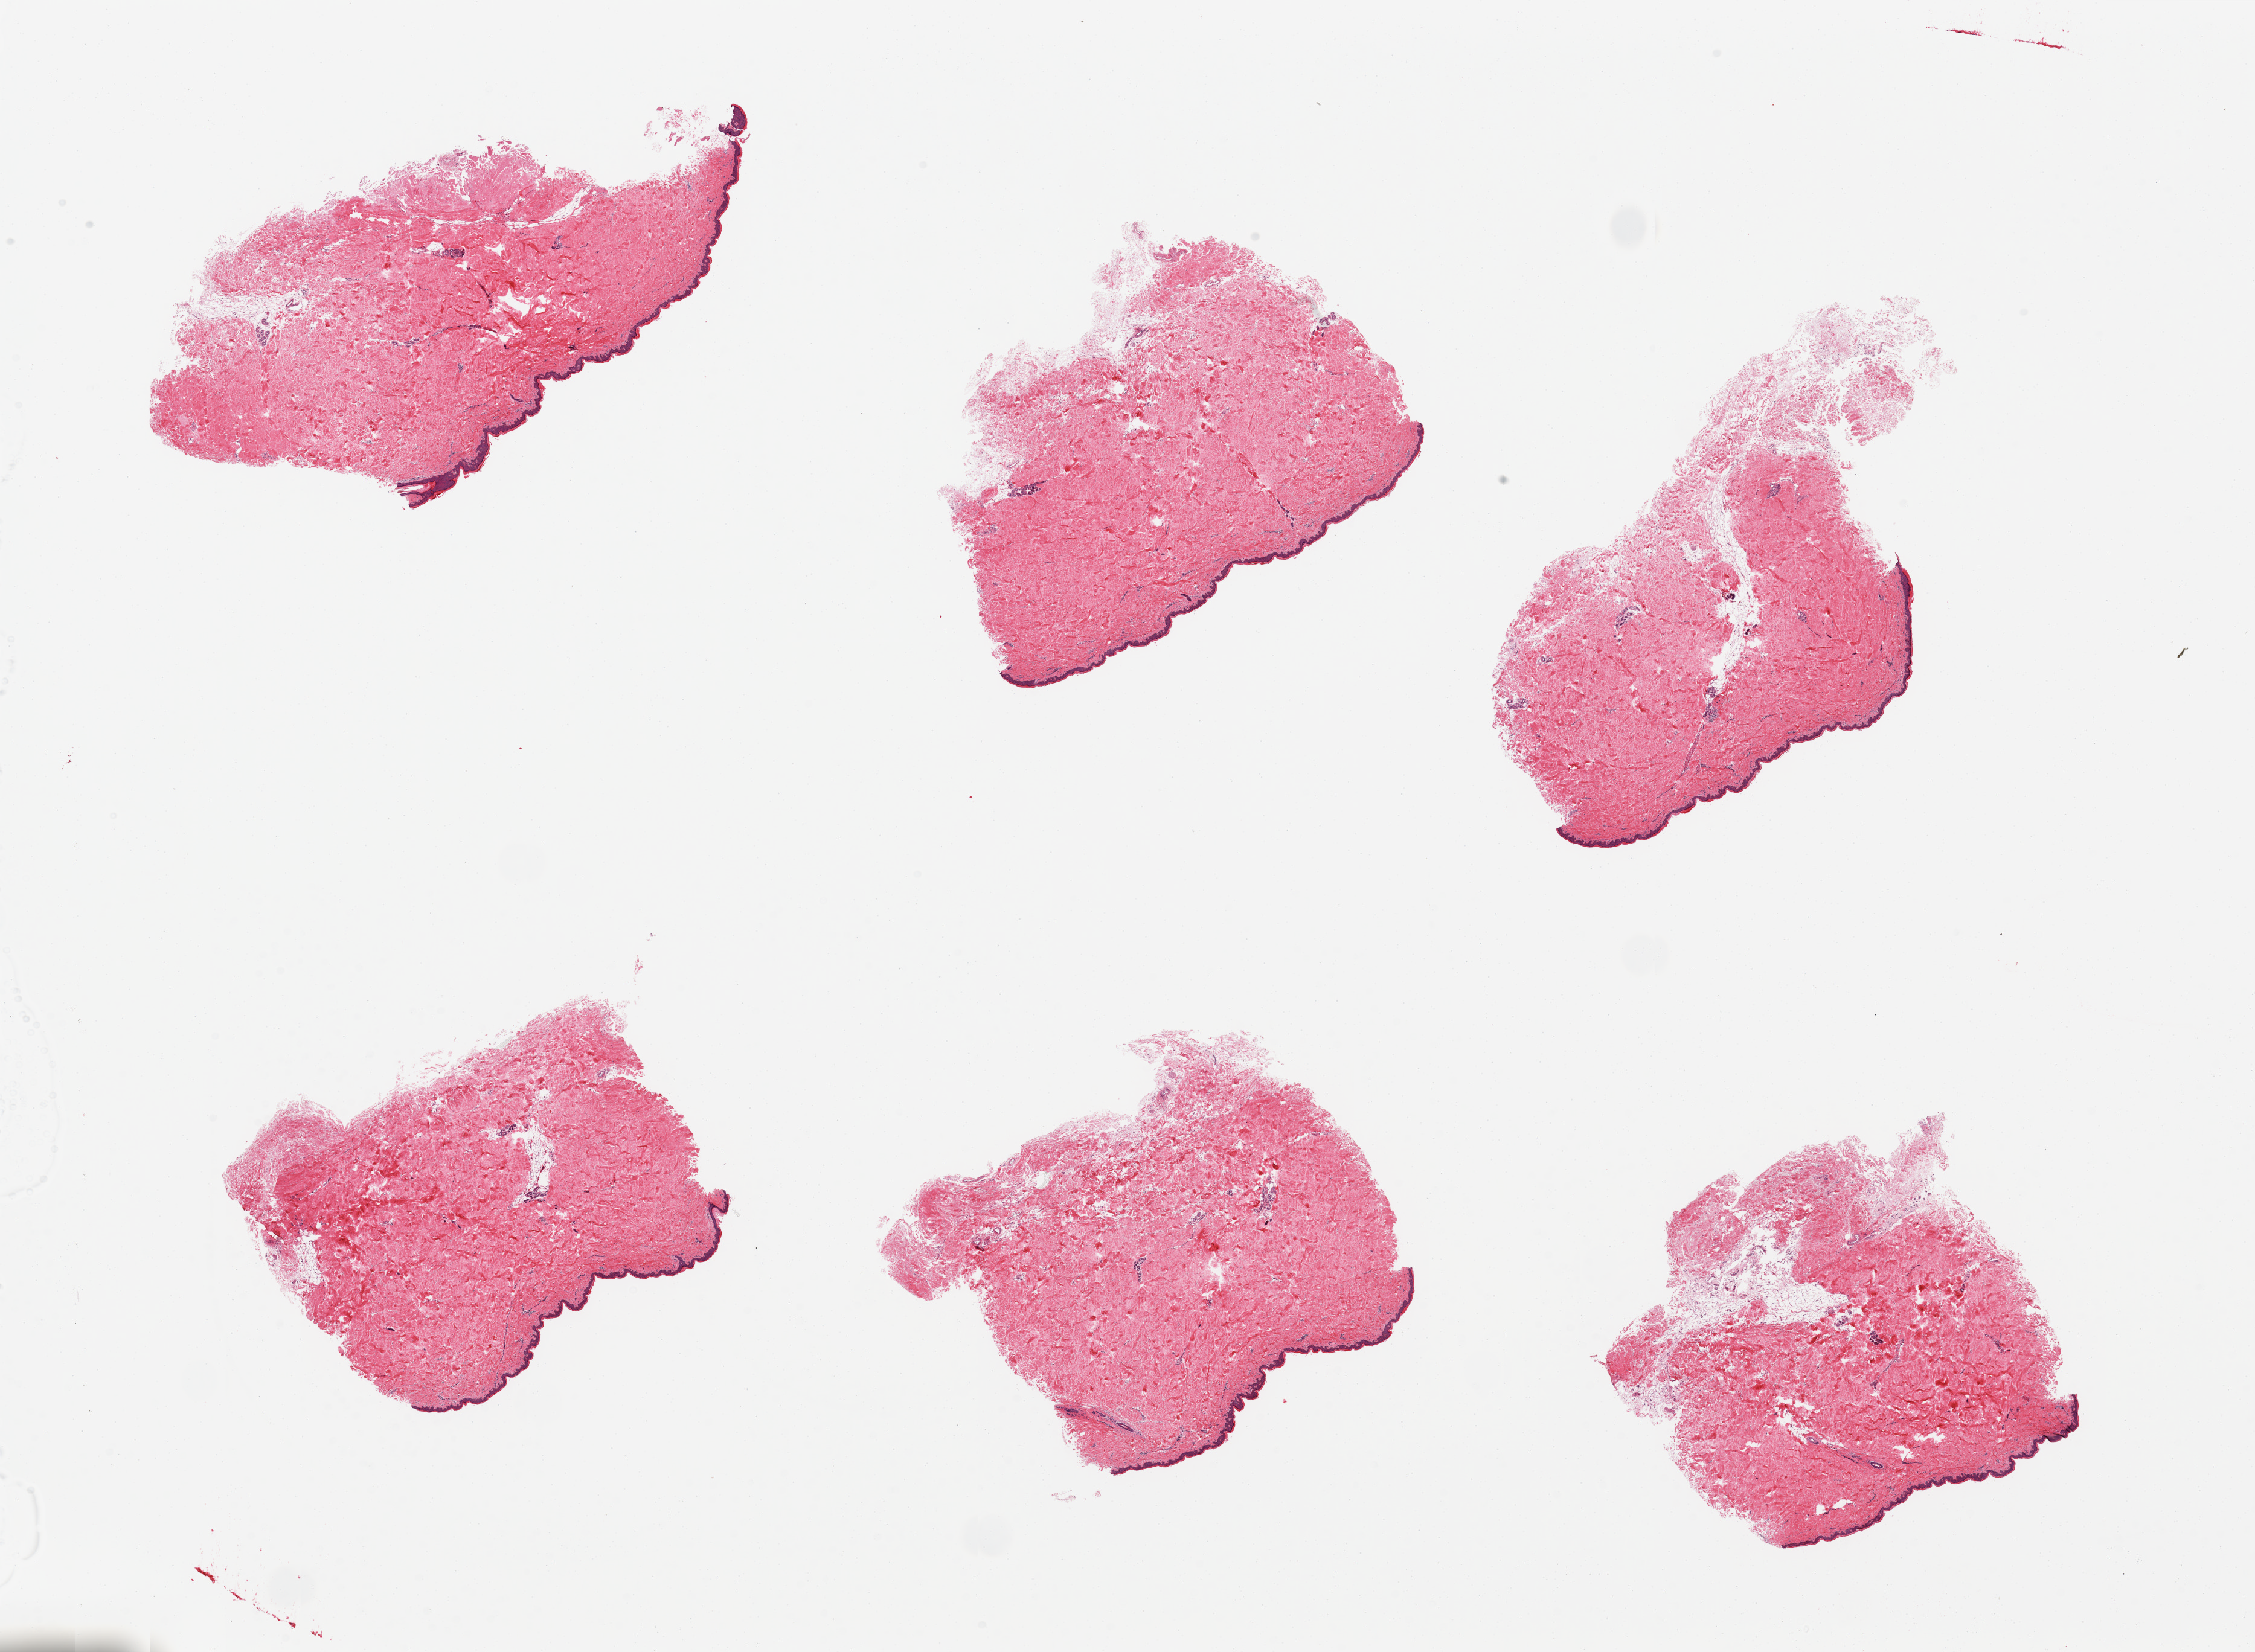
Whole-slide image, hematoxylin and eosin (H&E) stain — low-resolution overview of the scanned area, about 29.5 x 21.6 mm (acquisition: 20x scan); PAXgene-fixed, paraffin-embedded tissue; section of skin of suprapubic region (target tissue); tissue donor sample. Female donor.
- pathologist's review note for this sample: 6 pieces, predominantly well trimmed